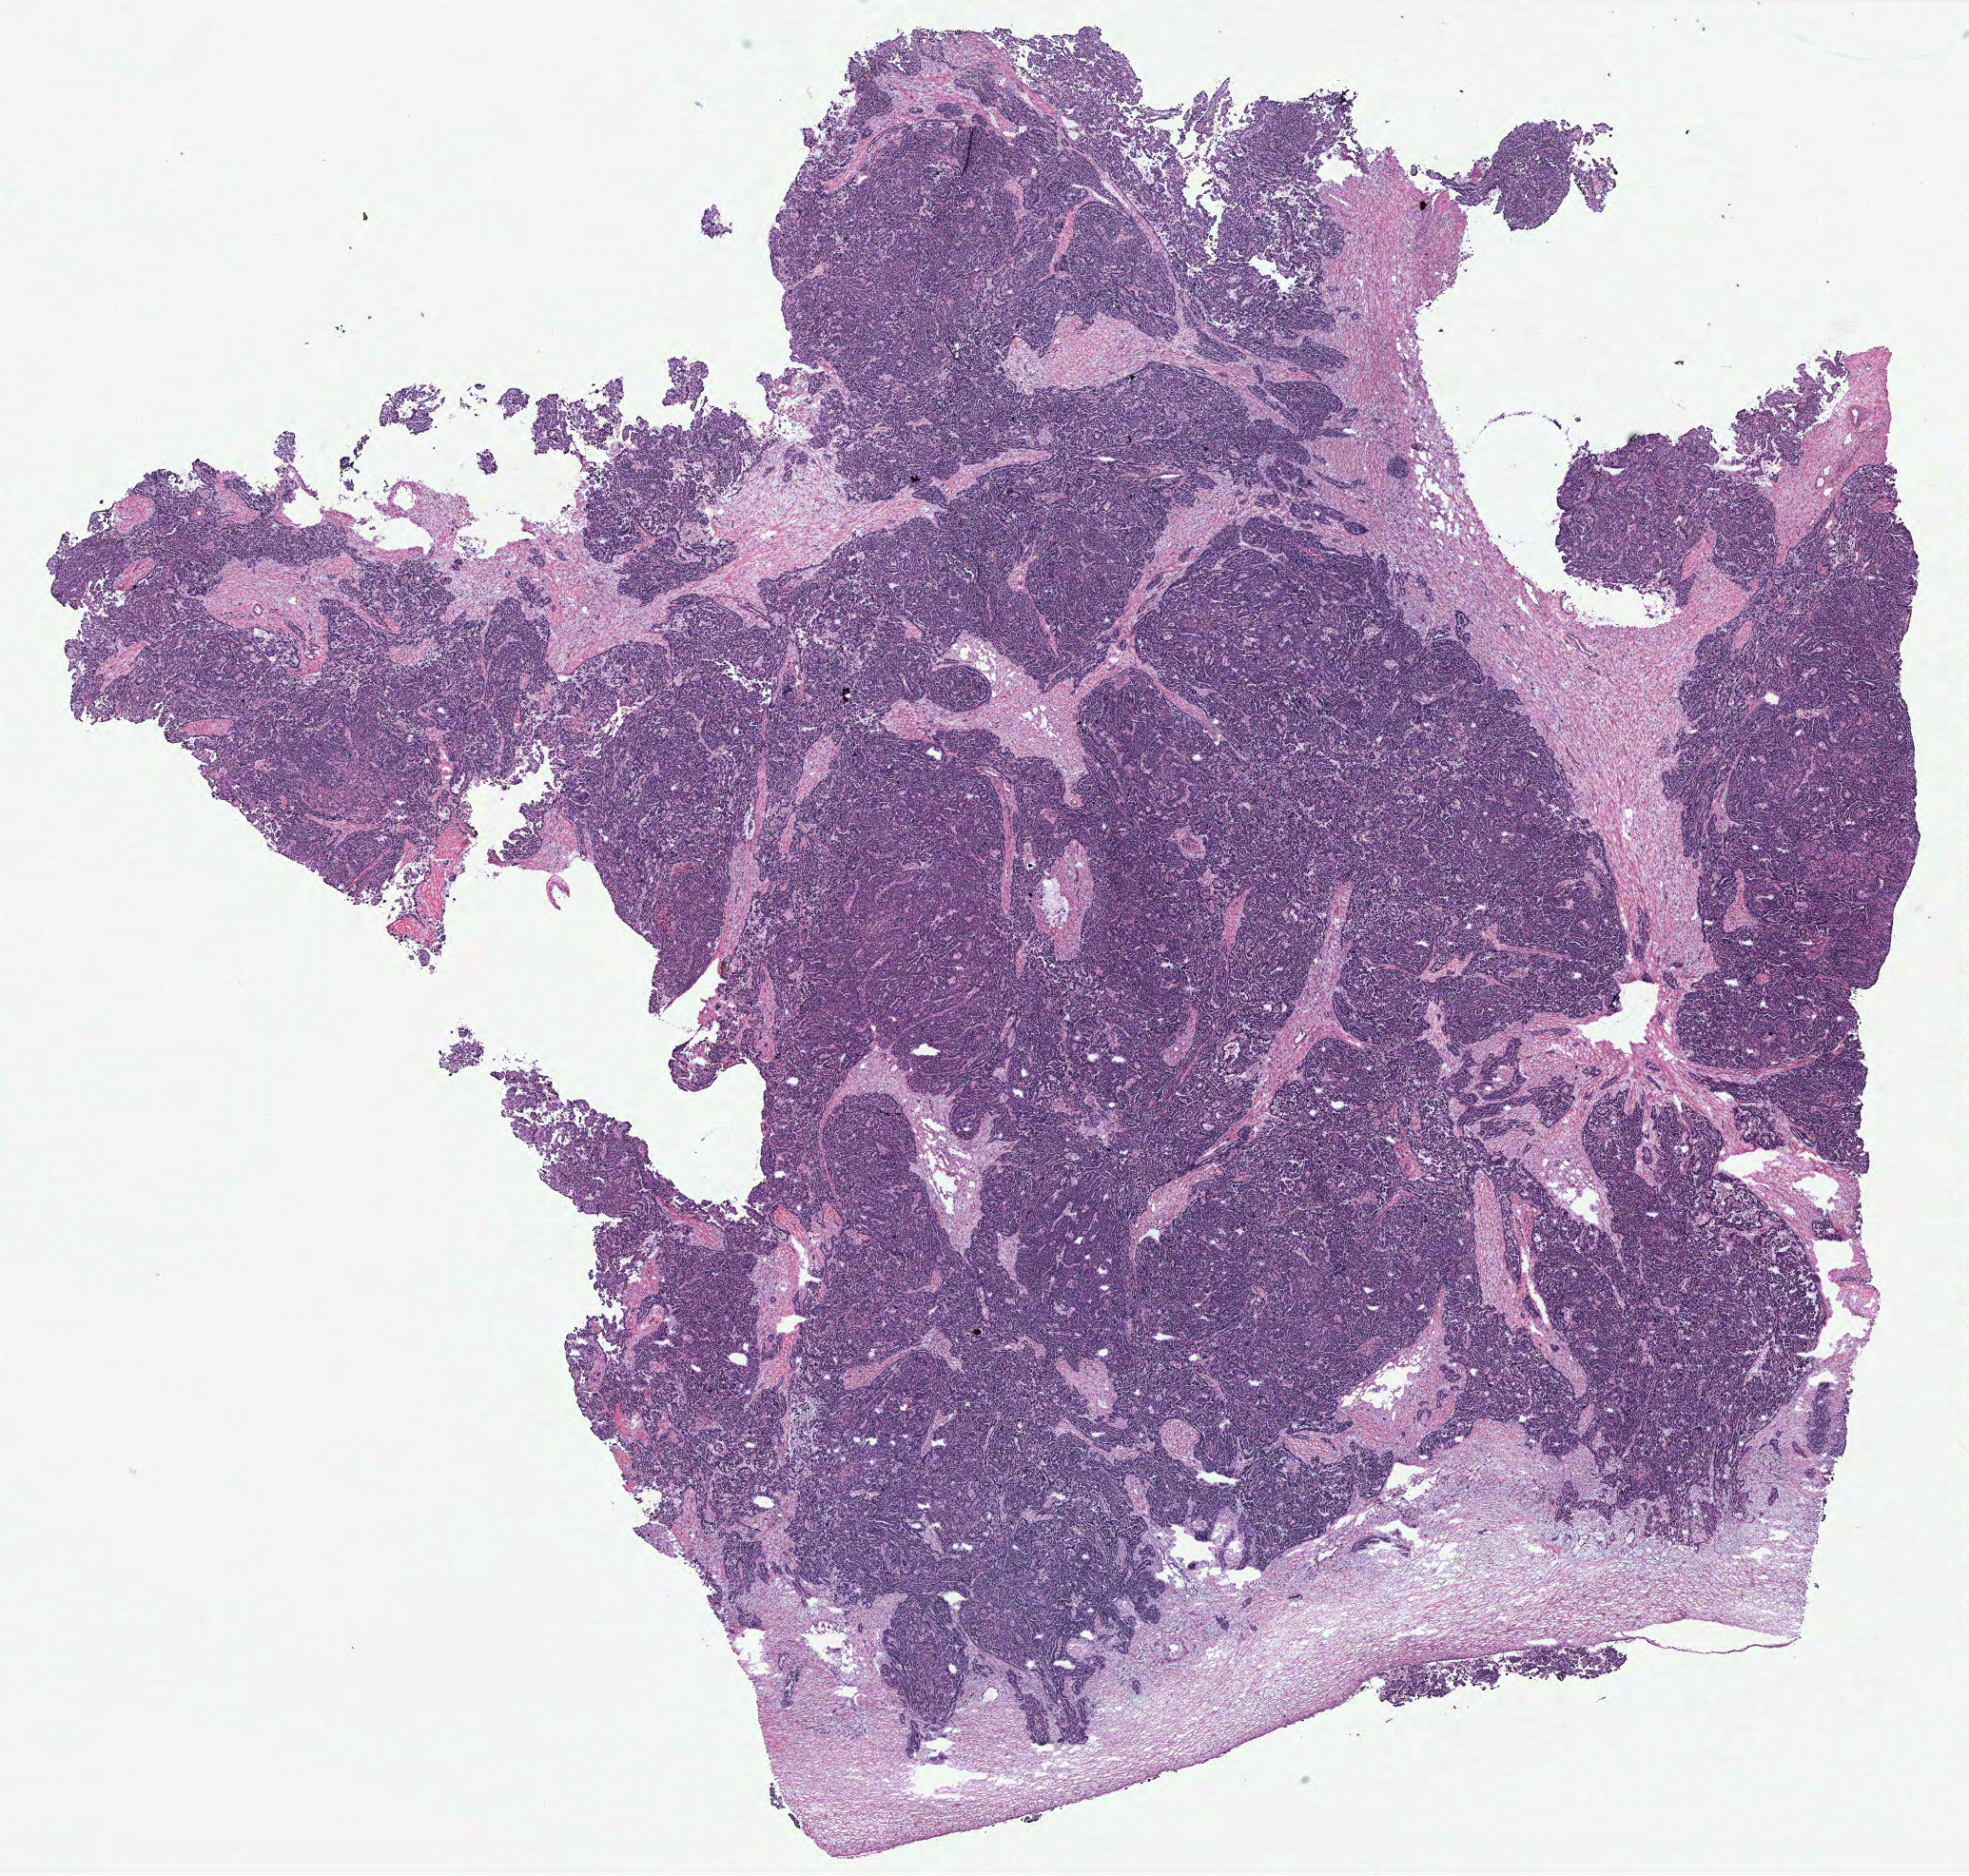
Hematoxylin and eosin (H&E) stained whole-slide image, shown as a low-resolution overview of the whole scanned area (about 16.6 x 15.8 mm), tumour tissue sample, ovary. 65-year-old female patient.
Histologic diagnosis: Serous adenocarcinoma, NOS.